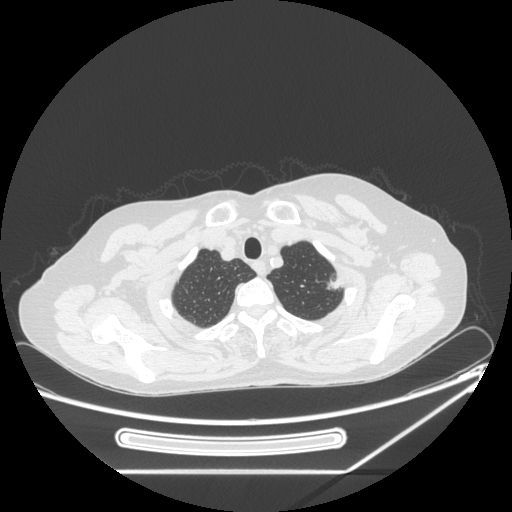
Chest CT, one axial slice; slice 214 of 250 in the series (ordered by position); 120 kVp; lung window (W 1500 / L -600 HU); 512 × 512 image matrix. Female patient, age 57 years. Case-level facts recorded for this patient, not image findings: clinical TNM (as recorded): T1c N0 M0; histopathological grade: G2-3.
Annotated regions visible in this slice (bounding box drawn by a radiologist):
- lung tumour (recorded histology: adenocarcinoma): bounding box (x1, y1, x2, y2) in pixels: (325, 273, 346, 295)